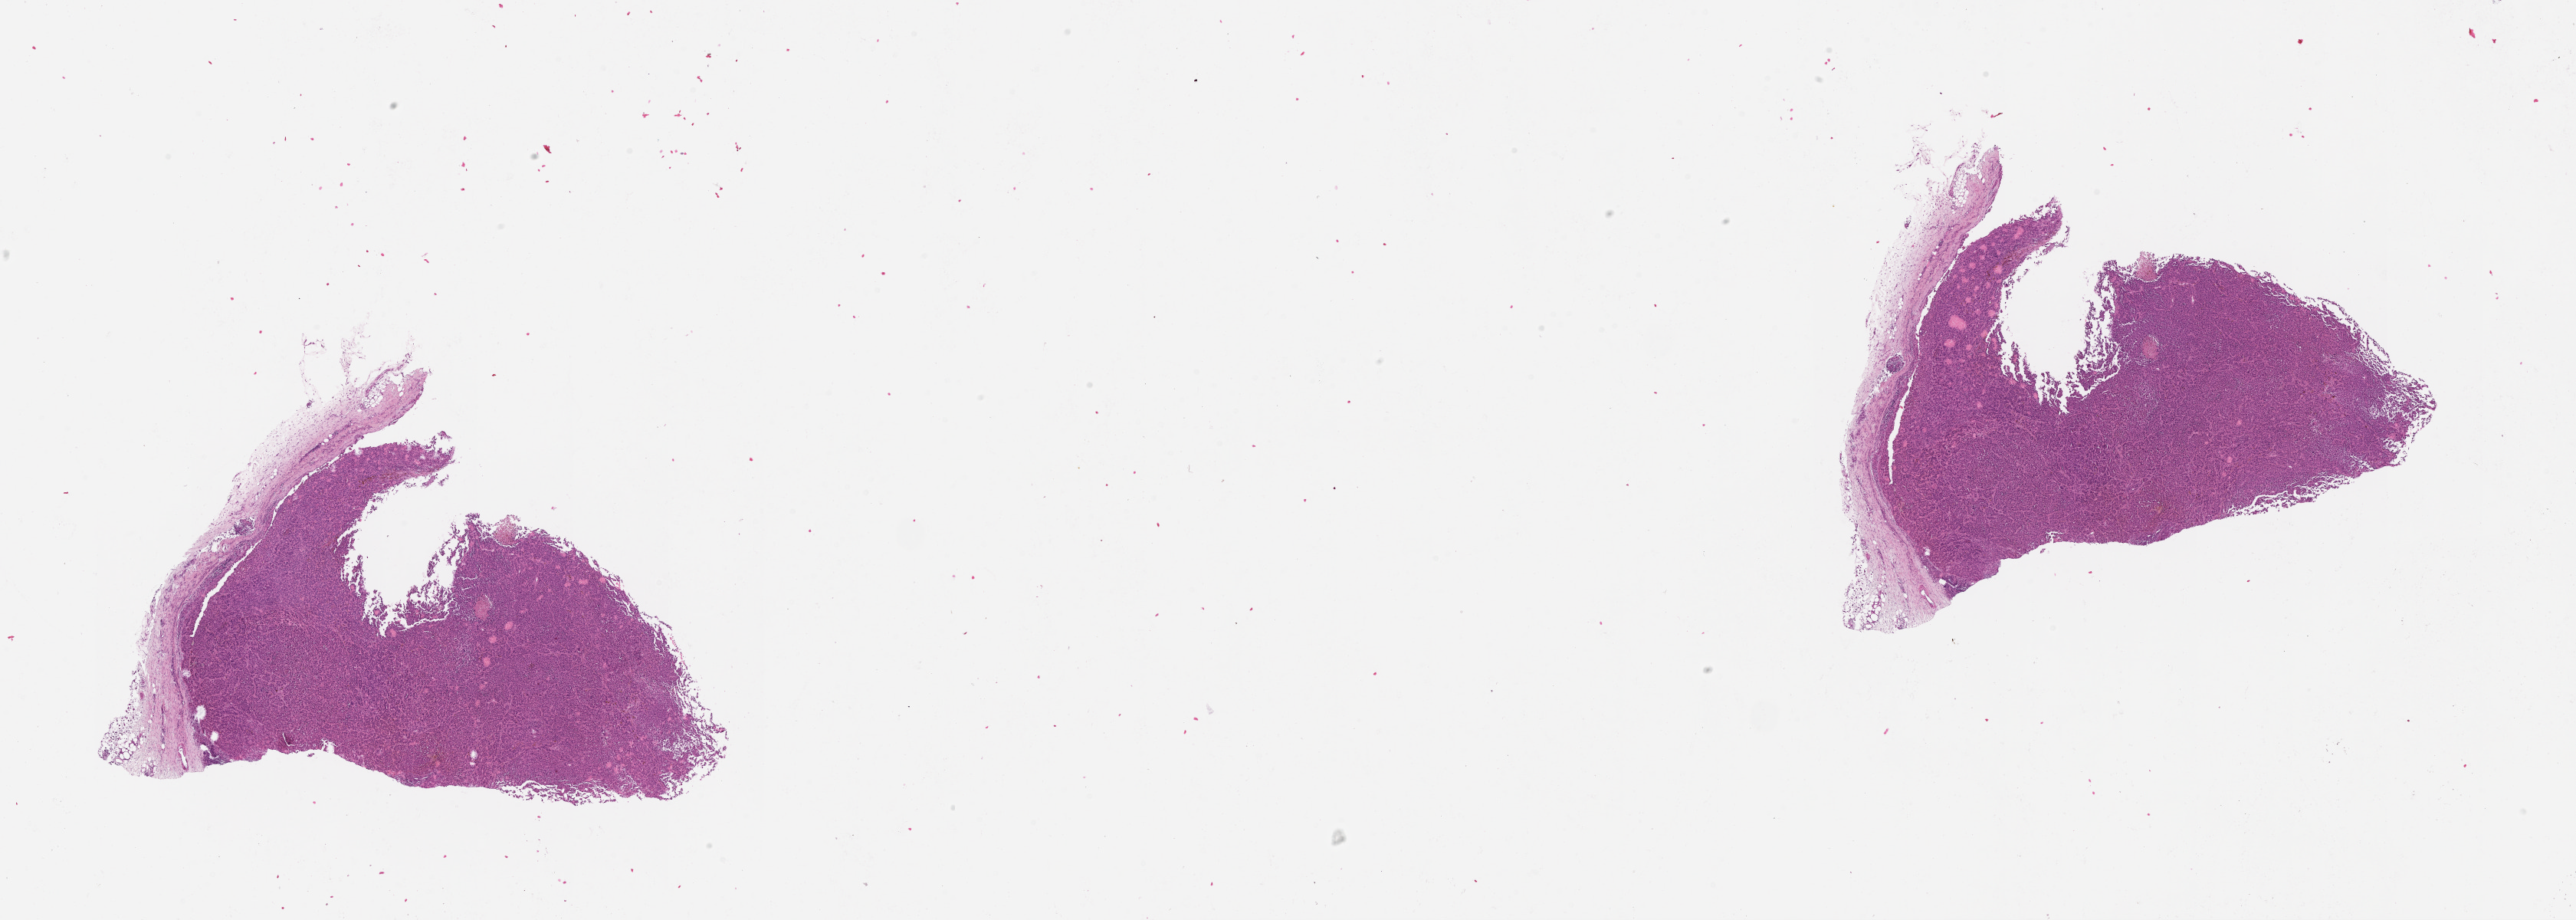
H&E whole-slide image — shown as a low-resolution overview of the whole scanned area (about 27.1 x 9.7 mm). Tumour tissue sample, sampled site: lymph node. Patient: male, age 72 years. Pathologist review of this section (percent, as recorded): tumour nuclei 80%, necrosis 0%.
• this section: metastatic tumour tissue
• patient diagnosis: Malignant melanoma, NOS